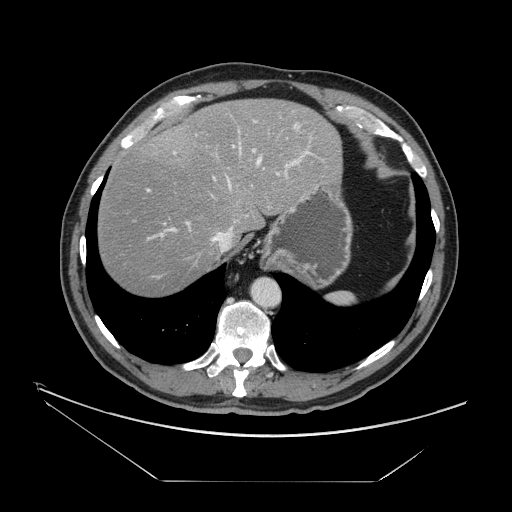
Contrast-enhanced abdominal CT, one axial slice. Position 126 of 161 along the scan axis. Reconstruction kernel STANDARD. 120 kVp. Intravenous contrast given. Soft-tissue window (W 400 / L 40 HU). 512 × 512 image matrix, field of view 440 × 440 mm. Male patient, age 65 years. From the clinical record (not read from this slice): diagnosis: colorectal cancer liver metastases, imaged before liver resection; multiple liver metastases: yes; largest metastasis: 4.2 cm; chemotherapy before resection: yes.
Annotated regions visible in this slice (manually delineated by an expert):
- hepatic veins: box from (x=210, y=126) to (x=264, y=252) px
- liver: (x=97, y=99)–(x=341, y=296)
- planned liver remnant (the part of the liver to remain after resection): (x=97, y=99)–(x=341, y=297)
- portal vein (with intrahepatic branches): (x=147, y=117)–(x=309, y=240)